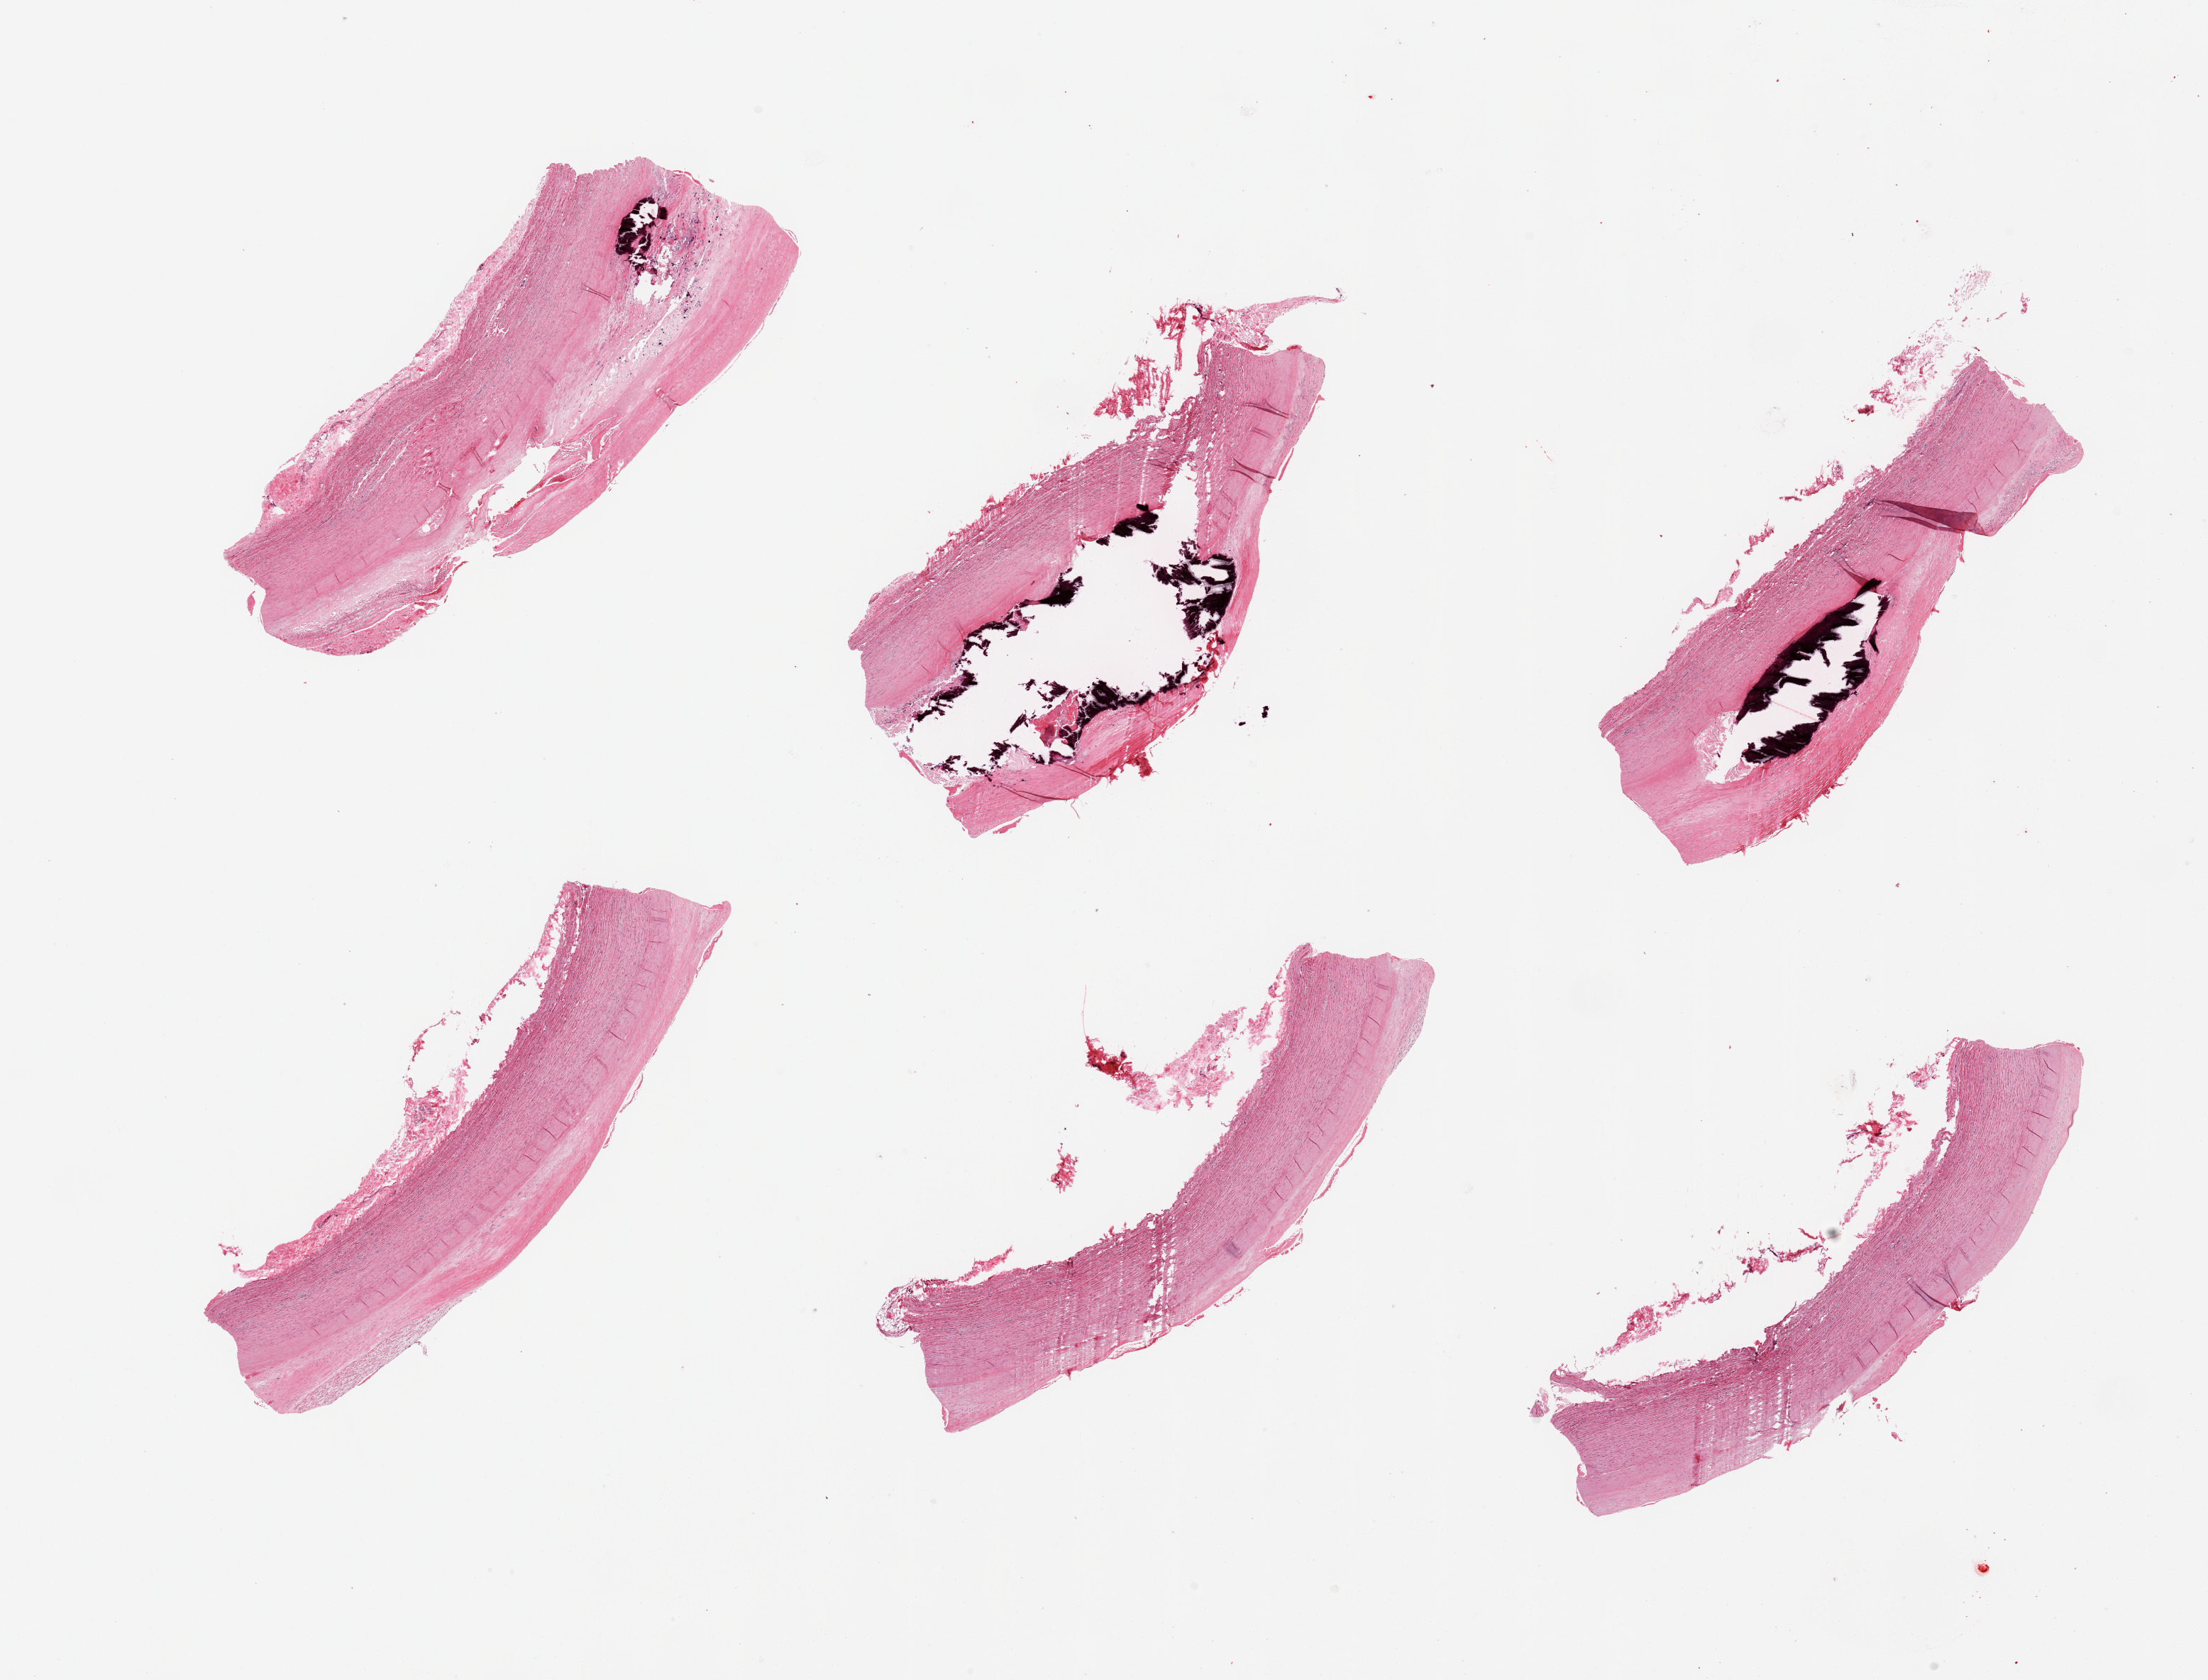
Whole-slide image, hematoxylin and eosin (H&E) stain, brightfield, low-resolution overview of the scanned area, about 24.6 x 18.7 mm (acquisition: 20x scan); PAXgene-fixed, paraffin-embedded tissue; target tissue: aorta; tissue donor sample. Donor sex: male.
- pathologist's review note for this sample: 6 pieces, calcifying atherosis up to ~2mm